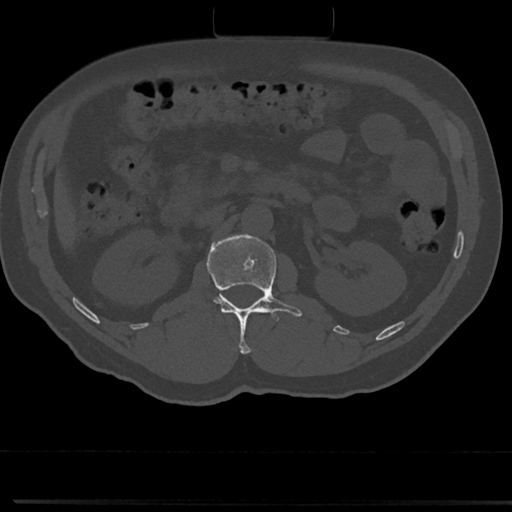
CT including the spine, one axial slice; slice 73 of 817 in the series (ordered by position); reconstruction kernel Br40s/3; bone window (W 1800 / L 400 HU); 512 × 512 image matrix, field of view 355 × 355 mm. Male patient, age 61 years. Case-level facts recorded for this patient, not image findings: primary cancer: prostate.
Outlined on this slice (semi-automatic segmentation, software-assisted and operator-edited):
- L1 vertebra: bounding box <202,235,302,353> (left, top, right, bottom; pixels)